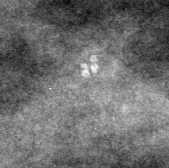
Cropped region of a digitized screen-film mammogram centred on a radiologist-marked abnormality; left breast; CC view.
- Marked abnormality: calcifications, morphology pleomorphic, distribution clustered; BI-RADS assessment category 4; pathology (as recorded): benign.